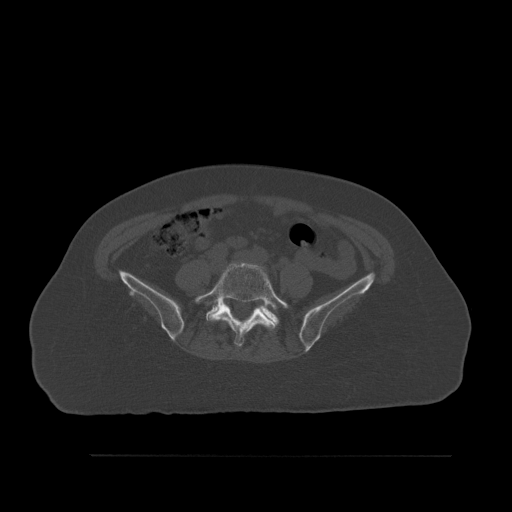
CT including the spine, one axial slice. Position 188 of 527 along the scan axis. Bone window (W 1800 / L 400 HU). 1.5 mm slice thickness. 512 × 512 image matrix, field of view 470 × 470 mm. Female patient, age 73 years. Case-level facts recorded for this patient, not image findings: primary cancer: breast.
Outlined on this slice (semi-automatic segmentation, software-assisted and operator-edited):
- L5 vertebra: bounding box (x1, y1, x2, y2) in pixels: (195, 263, 289, 347)